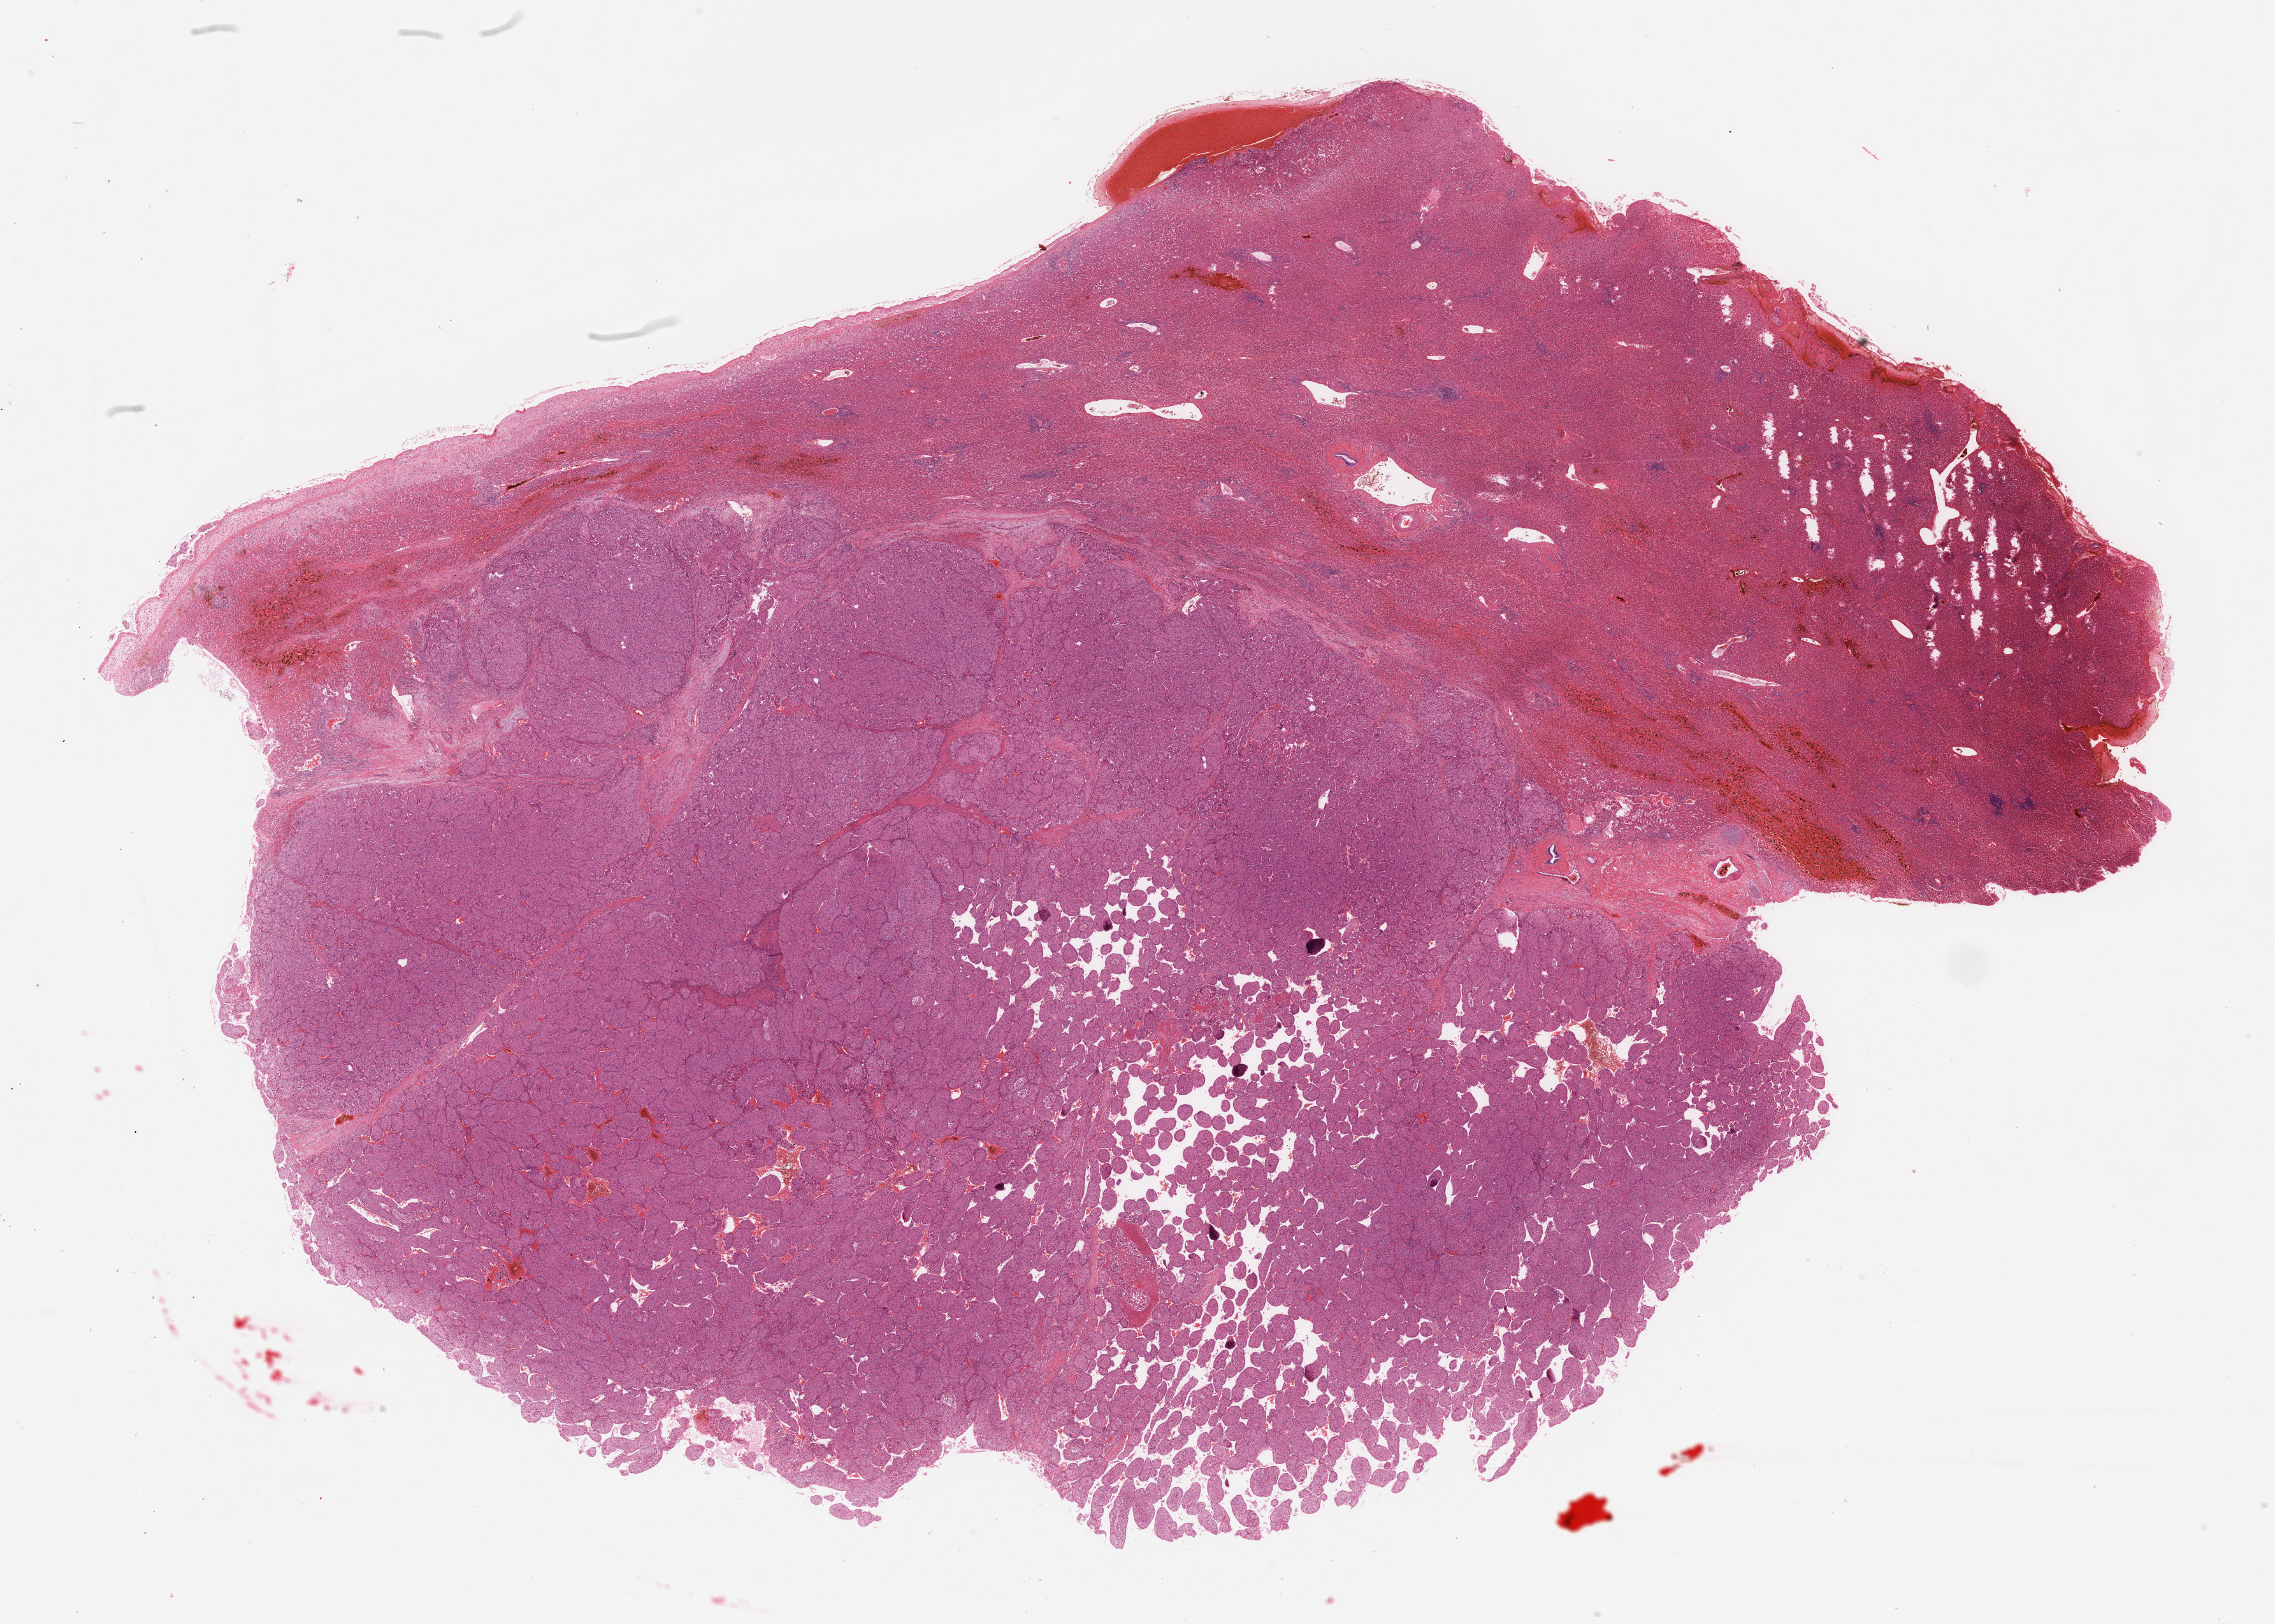
Whole-slide histology image, H&E-stained, a low-resolution overview of the entire scanned area, about 28.1 x 20.0 mm, formalin-fixed paraffin-embedded (FFPE) diagnostic section, primary tumour sample from the liver. Patient: male, age at initial diagnosis 47 years. Histologic grade: G2 (moderately differentiated).
AJCC pathologic stage: II (7th edition). Diagnosis: Hepatocellular carcinoma, NOS.